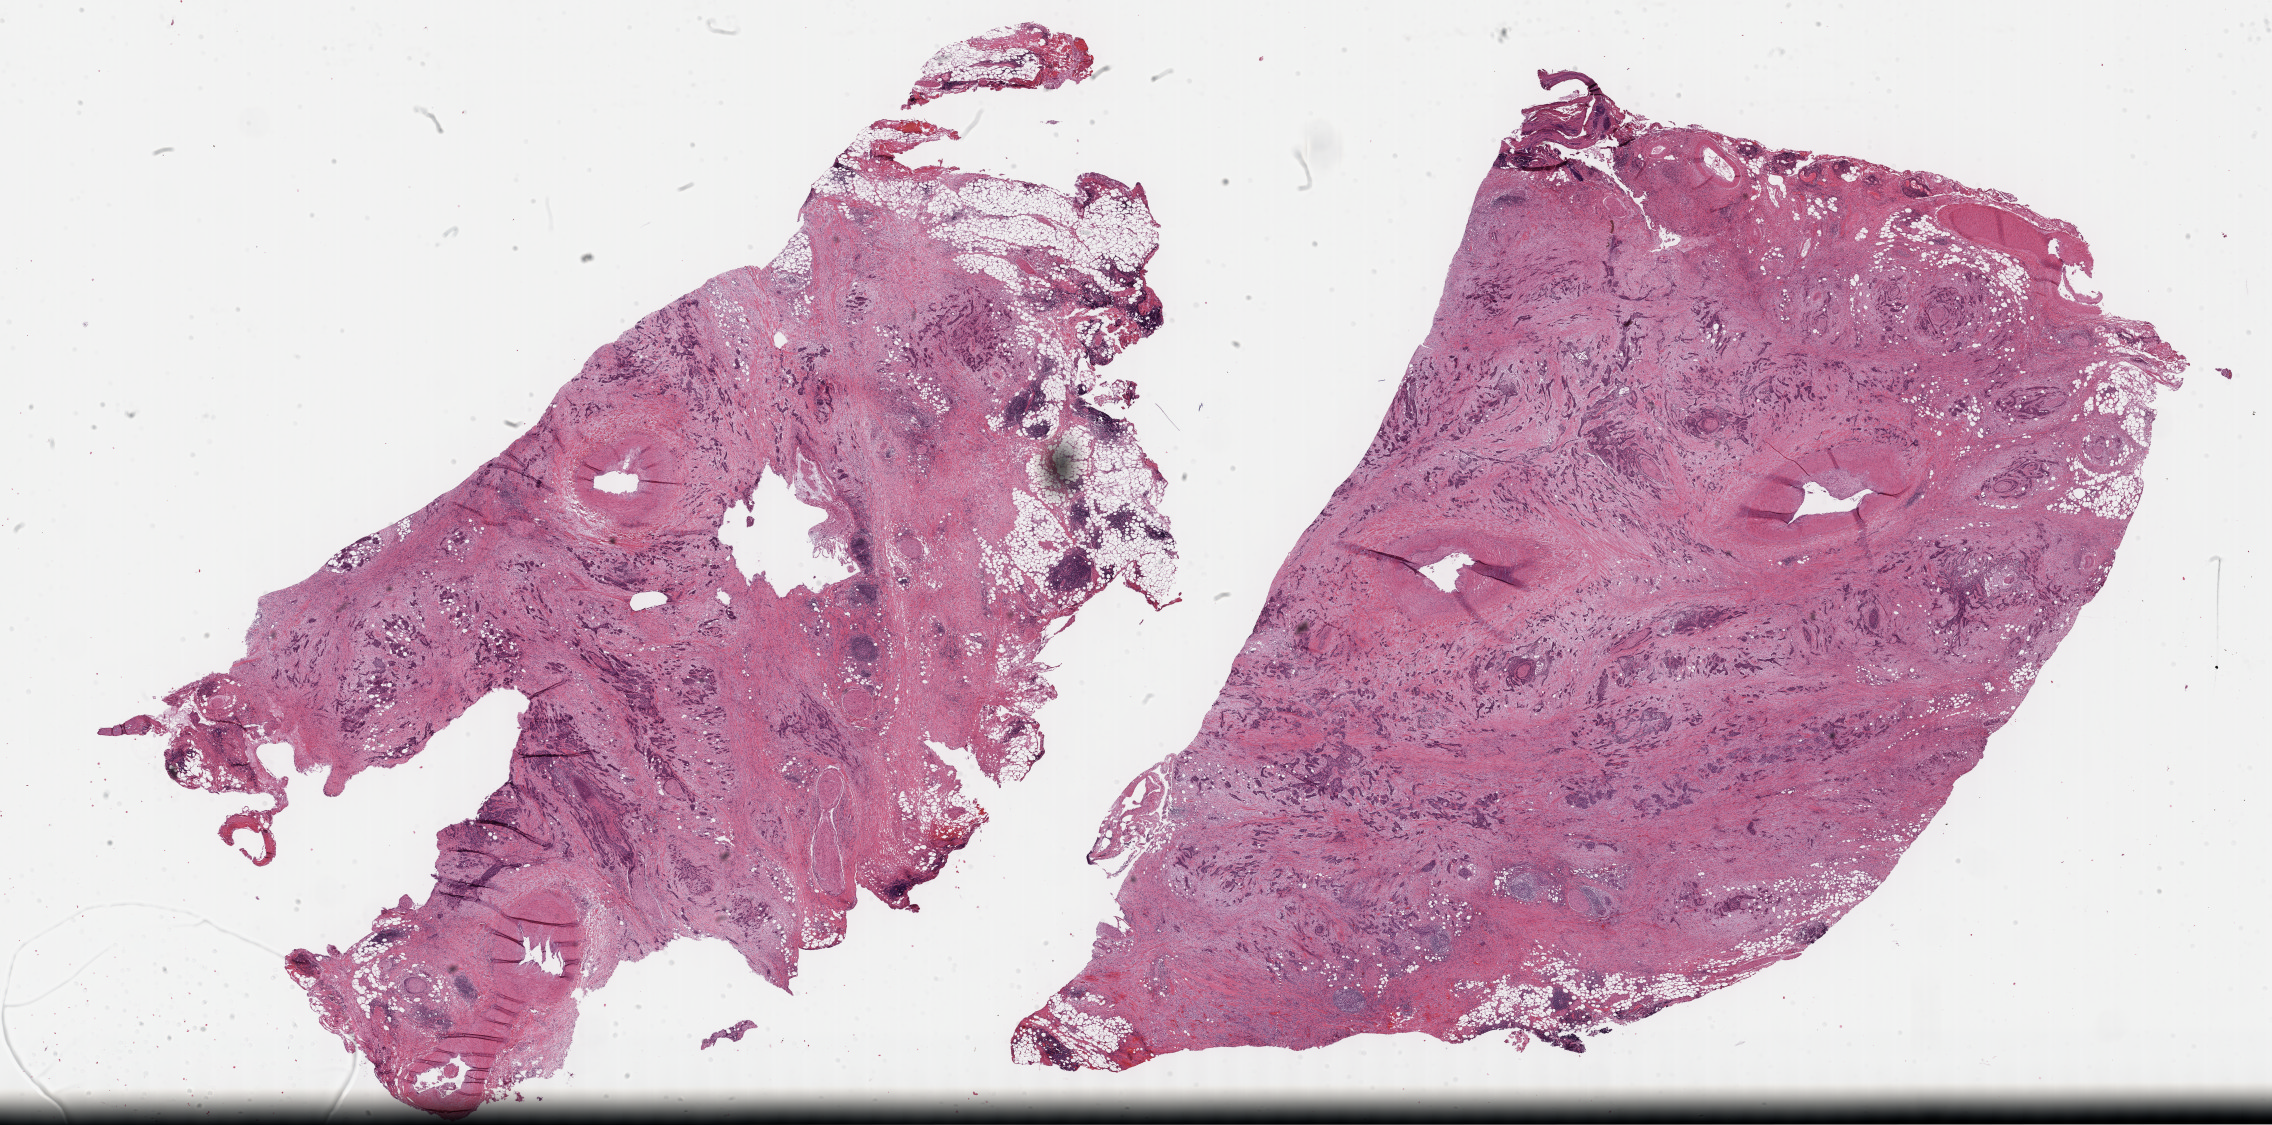
H&E whole-slide image, whole scanned area (about 36.7 x 18.2 mm, slide scanned at 40x) shown as a low-resolution overview. Formalin-fixed paraffin-embedded (FFPE) diagnostic section. Sample: primary tumour, pancreas. Female, age 55 years at initial diagnosis.
Diagnosis: Adenocarcinoma, NOS (head of pancreas).